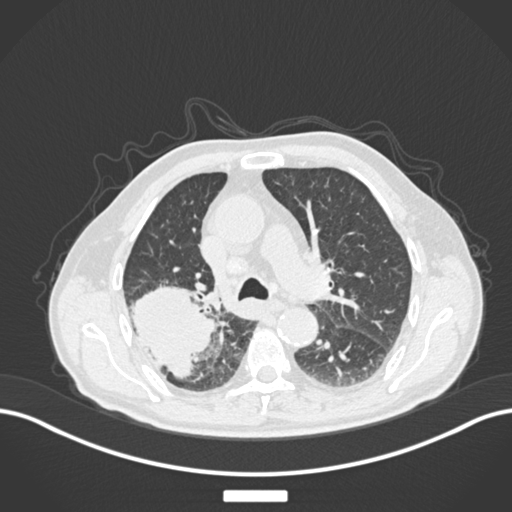
Chest CT, one axial slice; slice 116 of 201 in the series (ordered by position); lung window (W 1500 / L -600 HU); 1 mm slice thickness; 512 × 512 image matrix, field of view 400 × 400 mm. Male patient, age 72 years. From the clinical record (not read from this slice): clinical TNM (as recorded): T3 N2 M0.
Structures marked on this image (rectangle marked by the reading radiologist):
- lung tumour (recorded histology: adenocarcinoma): bounding box <128,280,219,386> (left, top, right, bottom; pixels)